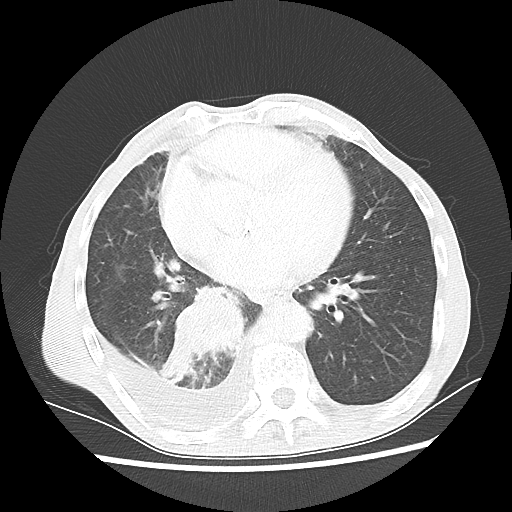
Chest CT, one axial slice; slice 25 of 60 in the series (ordered by position); reconstruction kernel LUNG; lung window (W 1500 / L -600 HU); 512 × 512 image matrix. Male patient, age 76 years. From the clinical record (not read from this slice): clinical TNM (as recorded): T3 N3 M1a; histopathological grade: G3.
Structures marked on this image (bounding box drawn by a radiologist):
- lung tumour (recorded histology: squamous cell carcinoma): bounding box <157,282,250,388> (left, top, right, bottom; pixels)